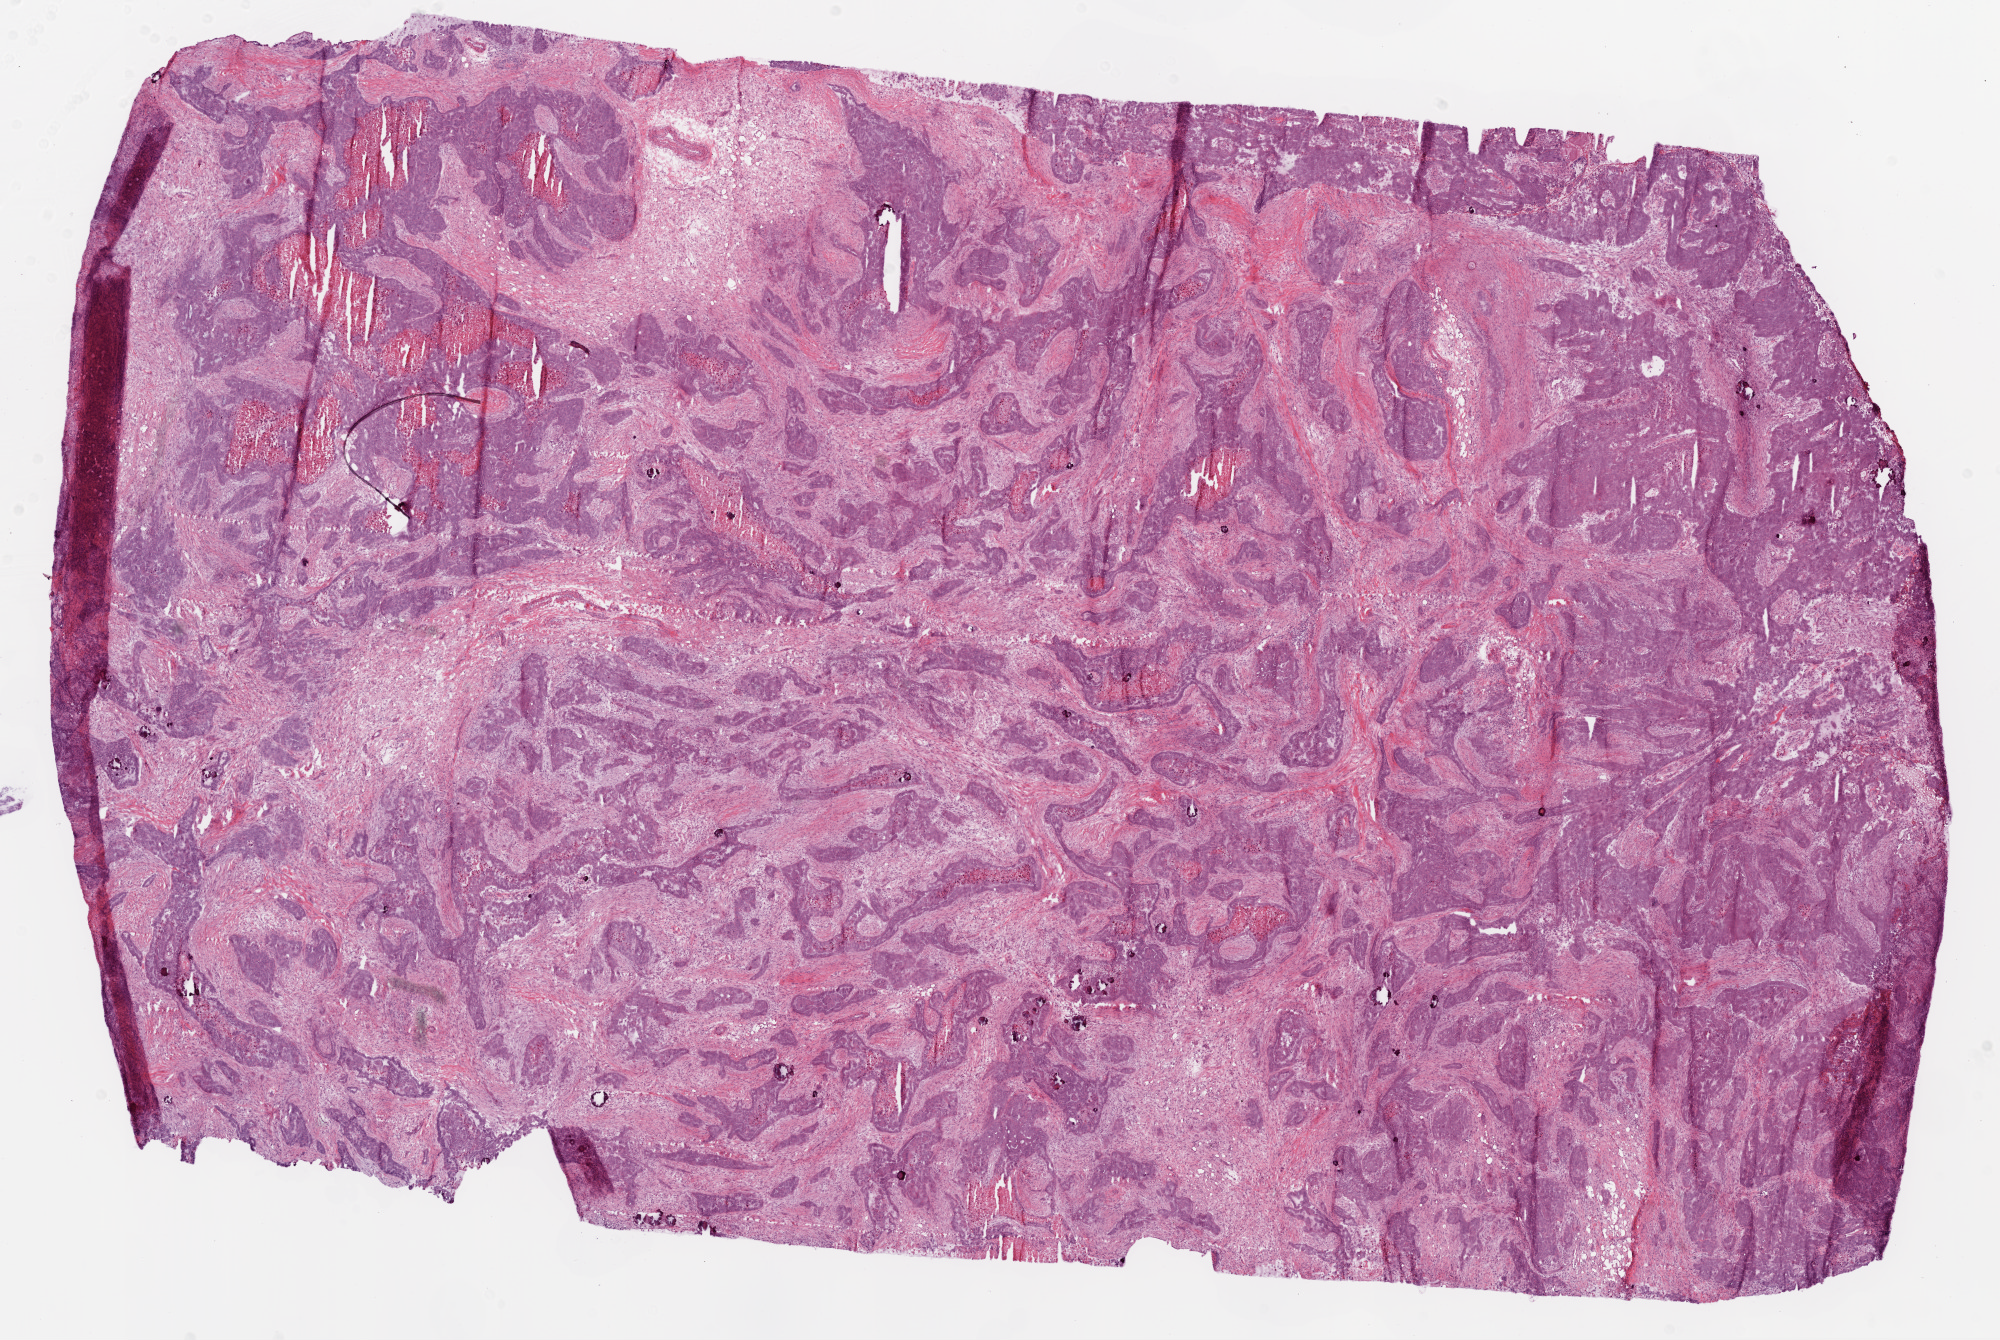
H&E whole-slide image — whole scanned area (about 16.0 x 10.8 mm, slide scanned at 20x) shown as a low-resolution overview; frozen section from the bottom of the tissue portion; primary tumour sample from the ovary. Patient: female, age at initial diagnosis 82 years. Composition of this section per pathologist review: tumour cells 45%, tumour nuclei 70%.
Histologic diagnosis: Serous cystadenocarcinoma, NOS.